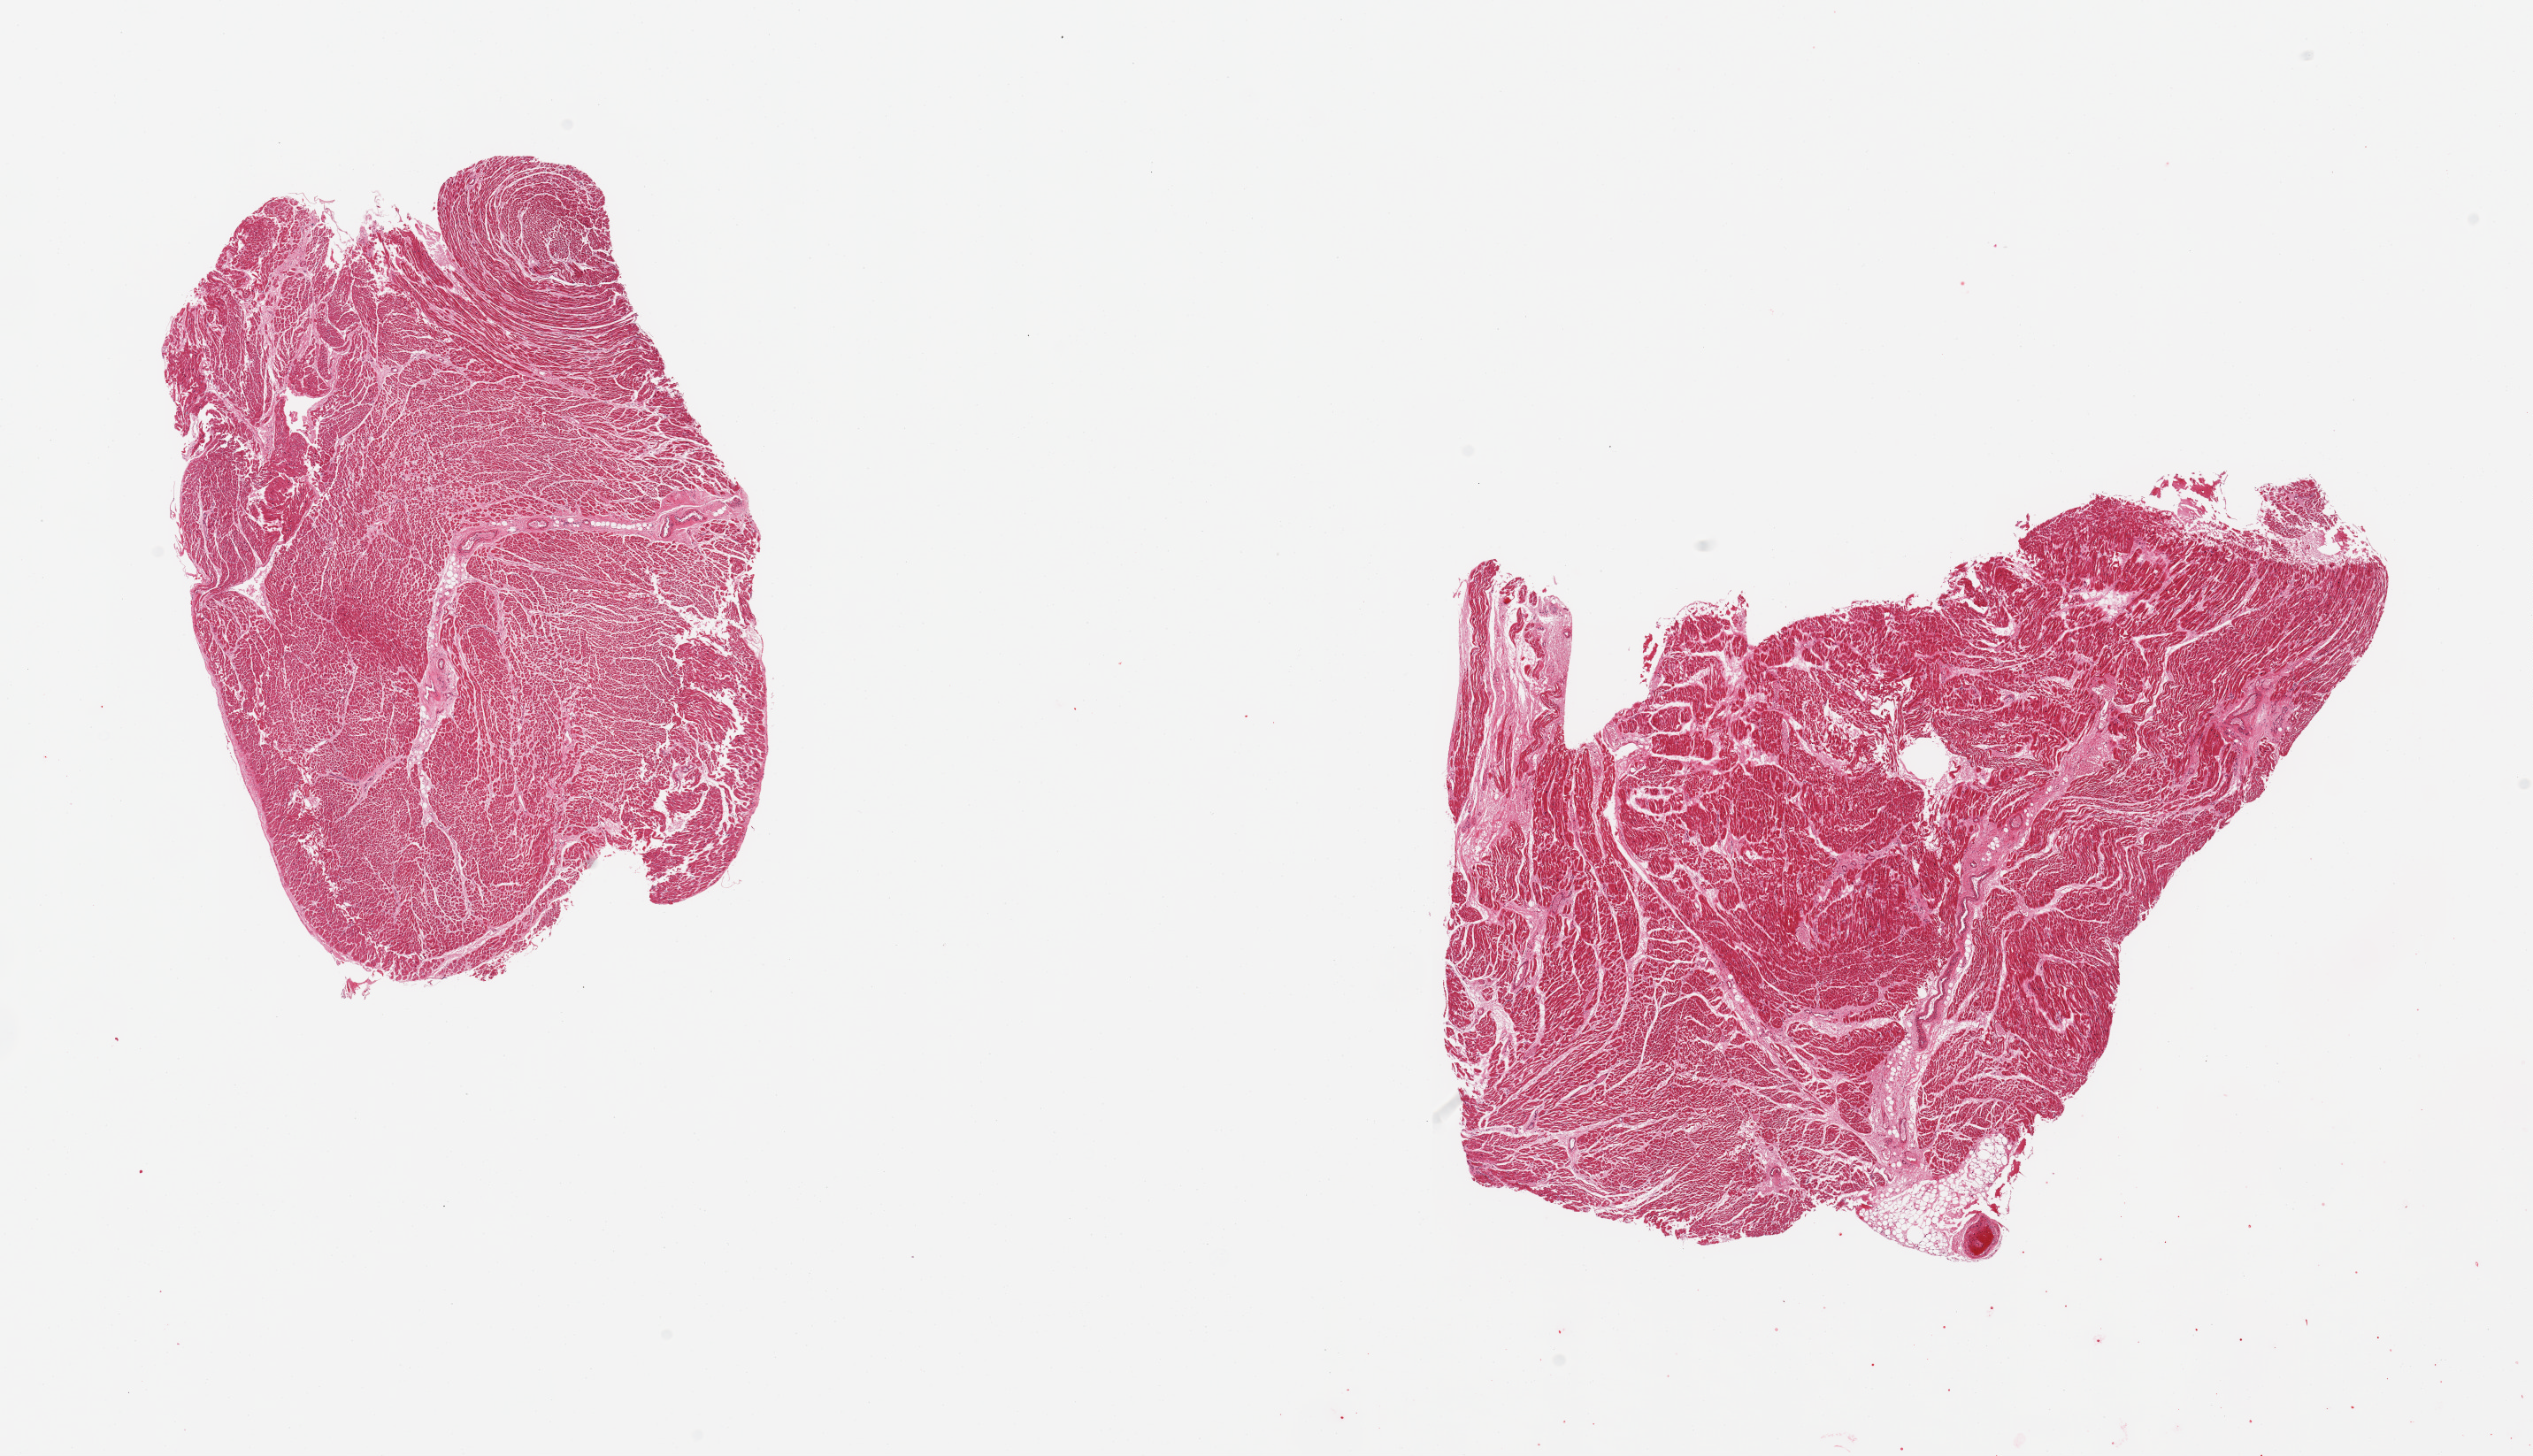
Haematoxylin and eosin whole-slide image, whole scanned area (about 22.6 x 13.0 mm) shown as a low-resolution overview; PAXgene-fixed paraffin-embedded (PFPE) section; target tissue: heart; donor tissue sample. Donor: male.
Reviewer comment on this tissue sample: 2 pieces, moderate interstitial fibrosis/chronic ischemic damage.